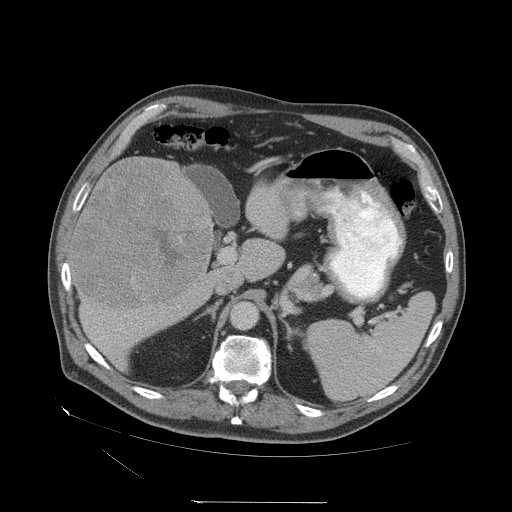
Contrast-enhanced abdominal CT (liver protocol), one axial slice; slice 31 of 83 in the series (ordered by position); soft-tissue window (W 400 / L 40 HU); 2.5 mm slice thickness; 512 × 512 image matrix, field of view 460 × 460 mm. From the clinical record (not read from this slice): diagnosis: hepatocellular carcinoma (patient treated with transarterial chemoembolisation; whether this scan precedes or follows treatment is not stated here); TNM stage (as recorded): Stage-I; Child-Pugh class: A; tumour differentiation: well differentiated; tumour nodularity: uninodular.
Outlined on this slice (semi-automatically segmented with operator editing):
- liver parenchyma outside the tumour (the mass and vessels are separate outlines, so this box may not span the whole liver): bounding box [x1, y1, x2, y2] px = [68, 156, 214, 370]
- mass: [71, 157, 211, 308]